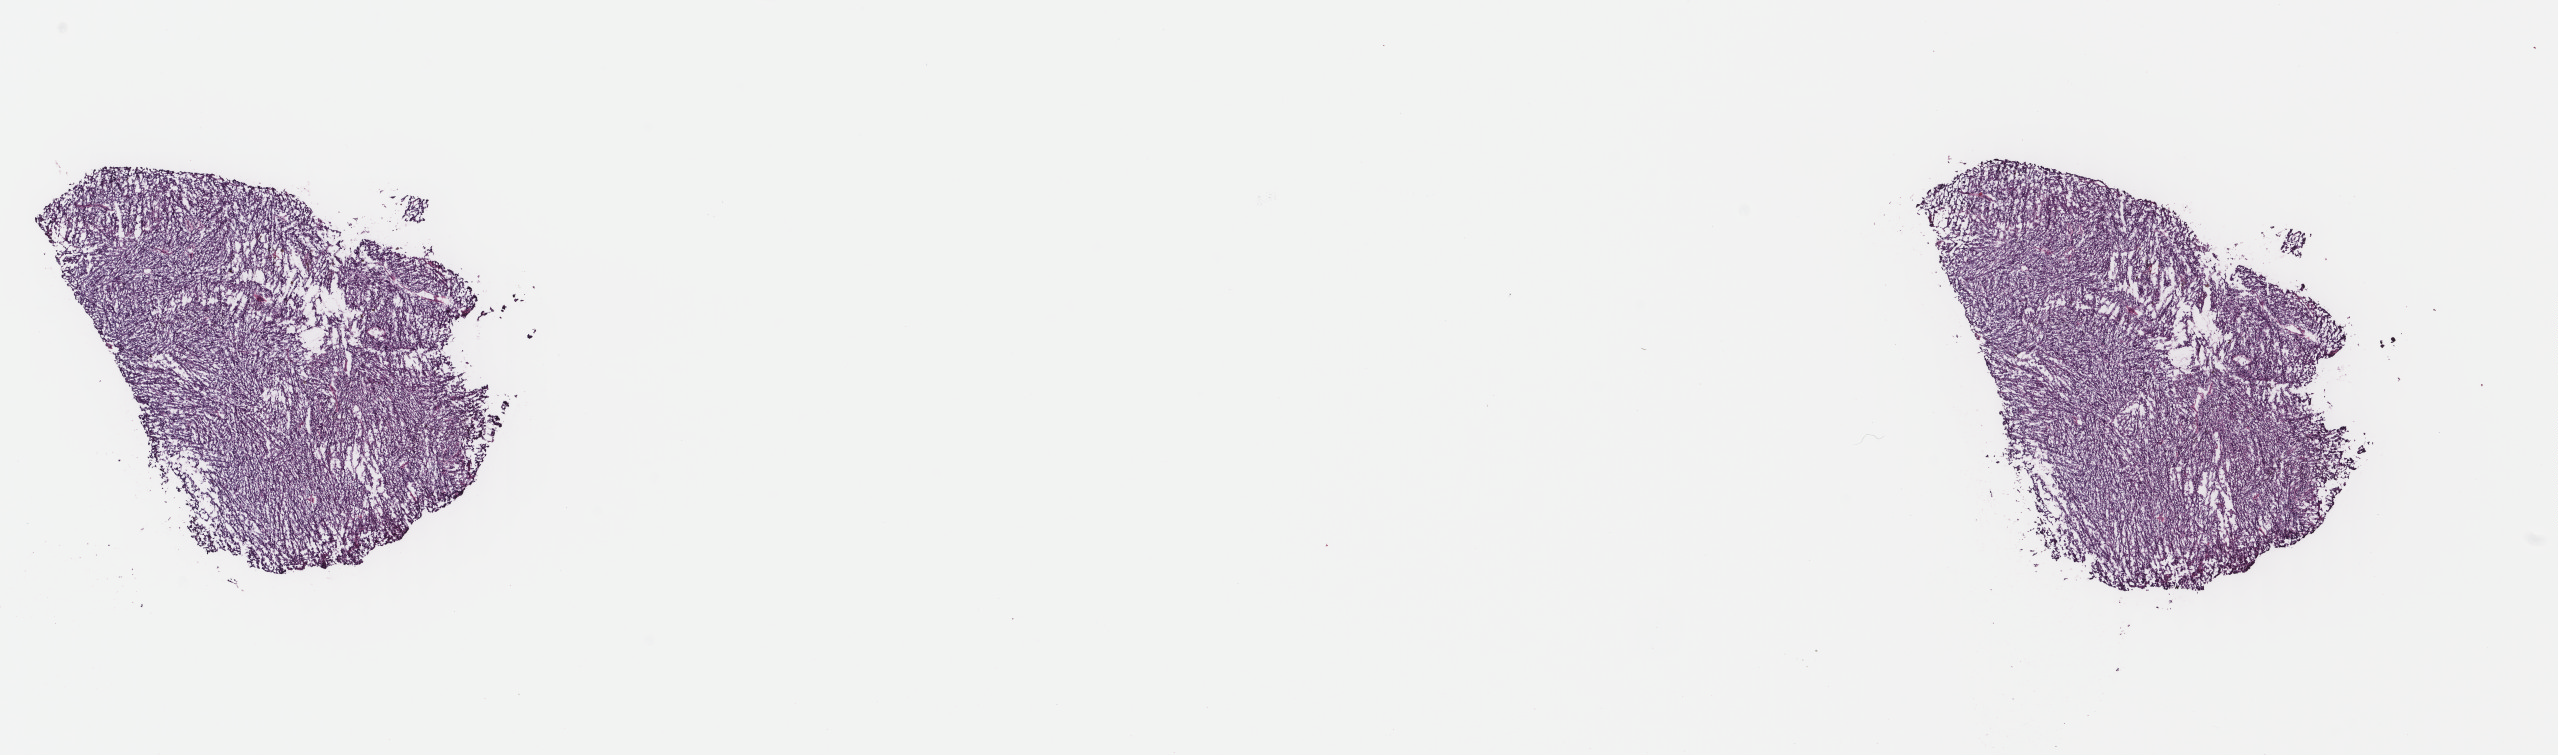
Whole-slide histology image, H&E, low-resolution overview of the scanned area, about 20.3 x 6.0 mm (from a 40x scan); frozen section from the top of the tissue portion; metastatic tumour sample, sampled site: lymph nodes of inguinal region or leg. Female, age 52 years at initial diagnosis. Pathologist review of this section (percent, as recorded): tumour cells 100%, tumour nuclei 96%.
This section: metastatic tumour tissue. Patient diagnosis: Malignant melanoma, NOS.